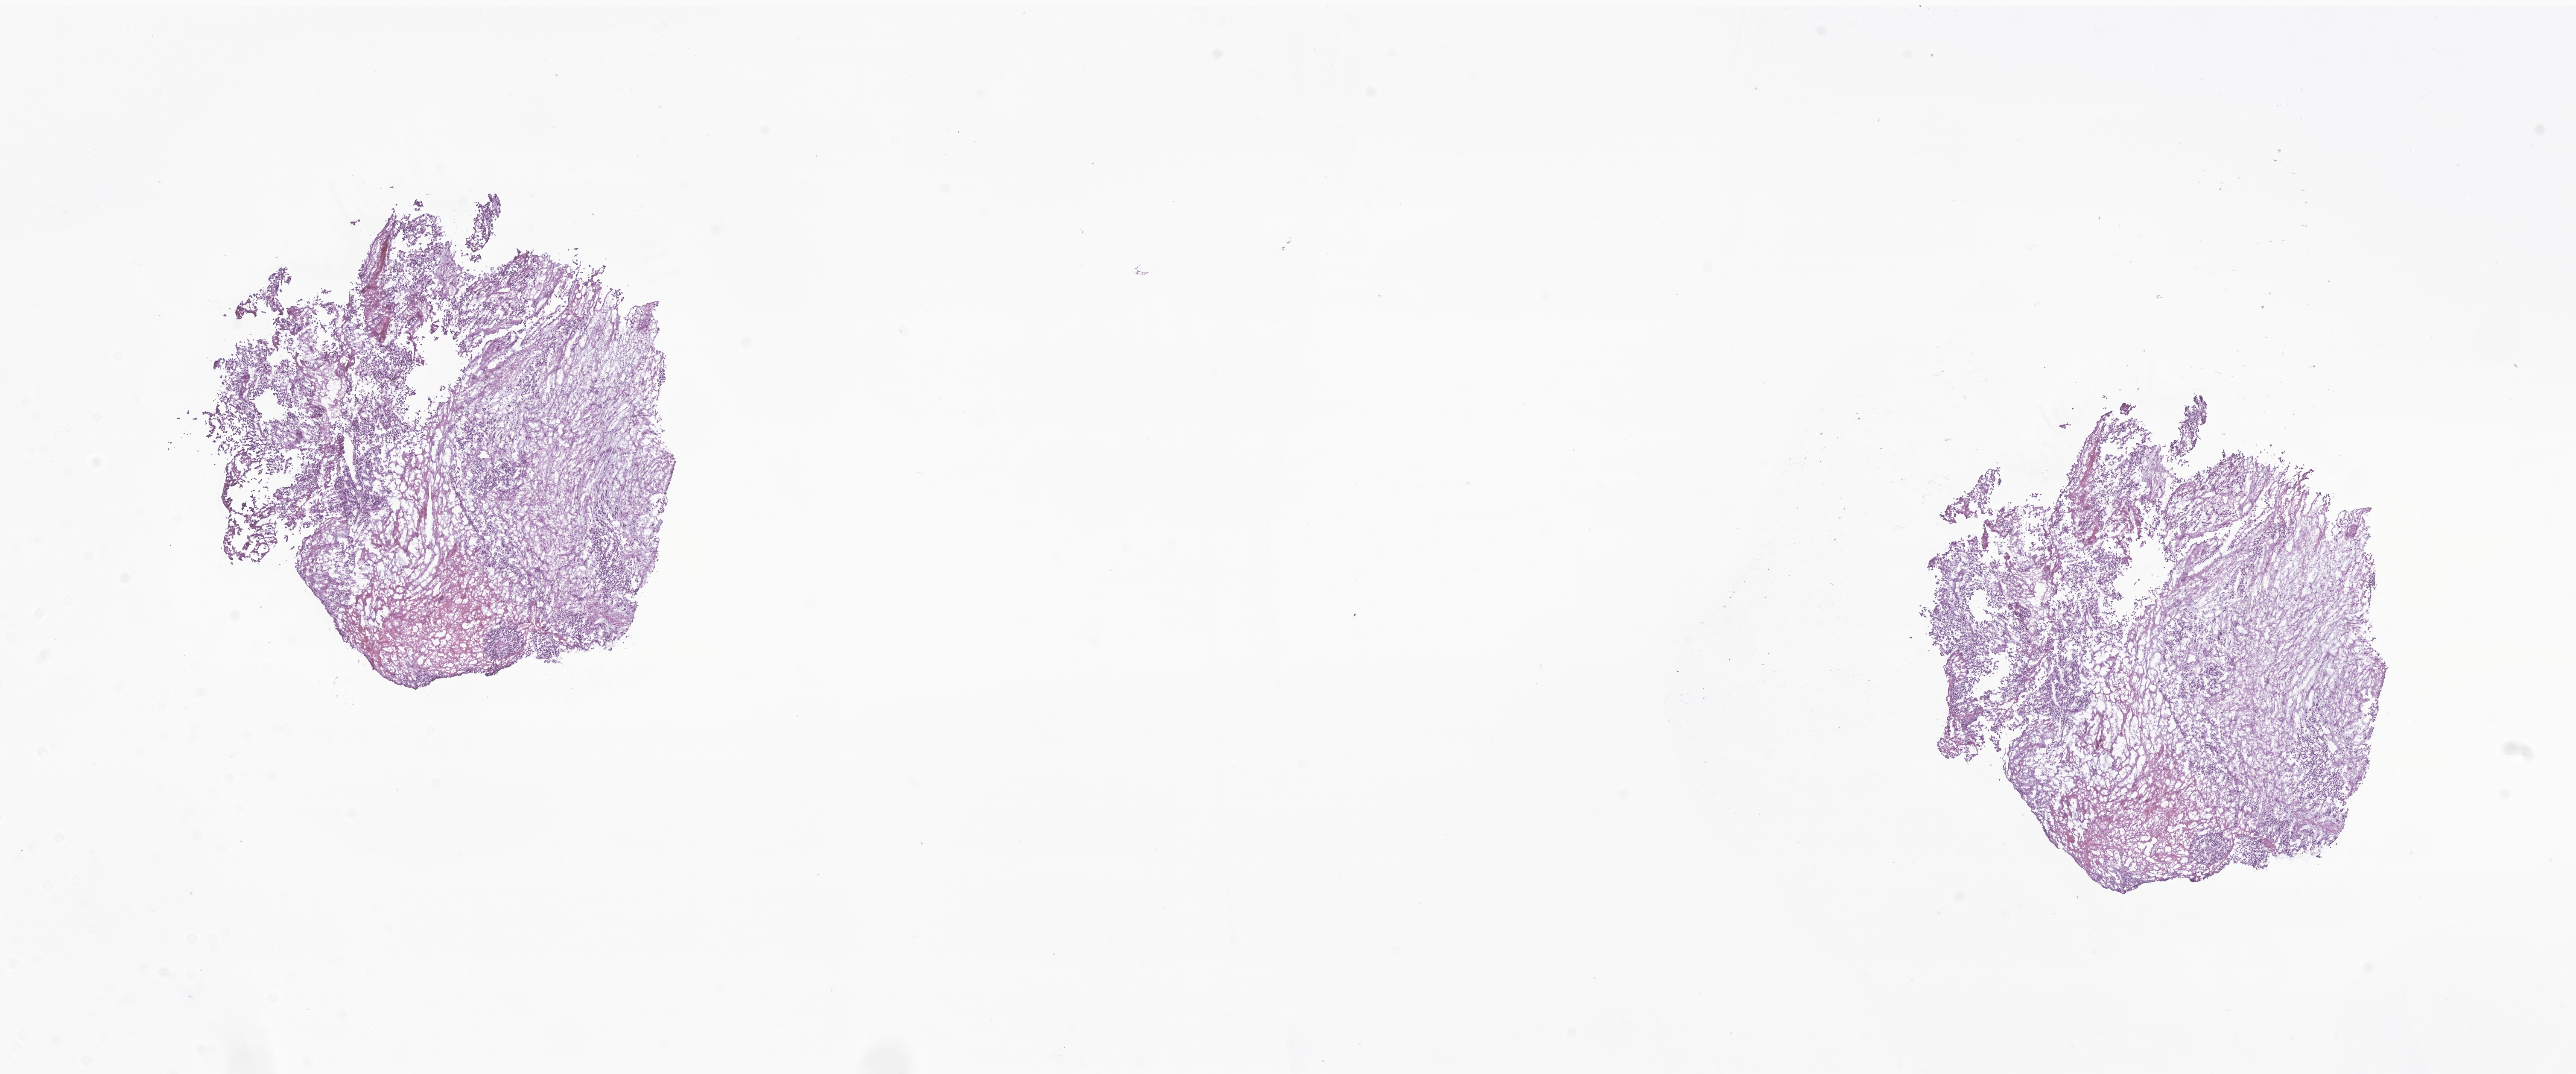
Digitized hematoxylin and eosin (H&E)-stained section of tumor tissue from the adrenal gland — low-resolution overview of the scanned area, about 25.4 x 10.6 mm, frozen section (OCT-embedded). Female patient, age 199 months (16 years 7 months).
* diagnosis: Adrenal cortical carcinoma